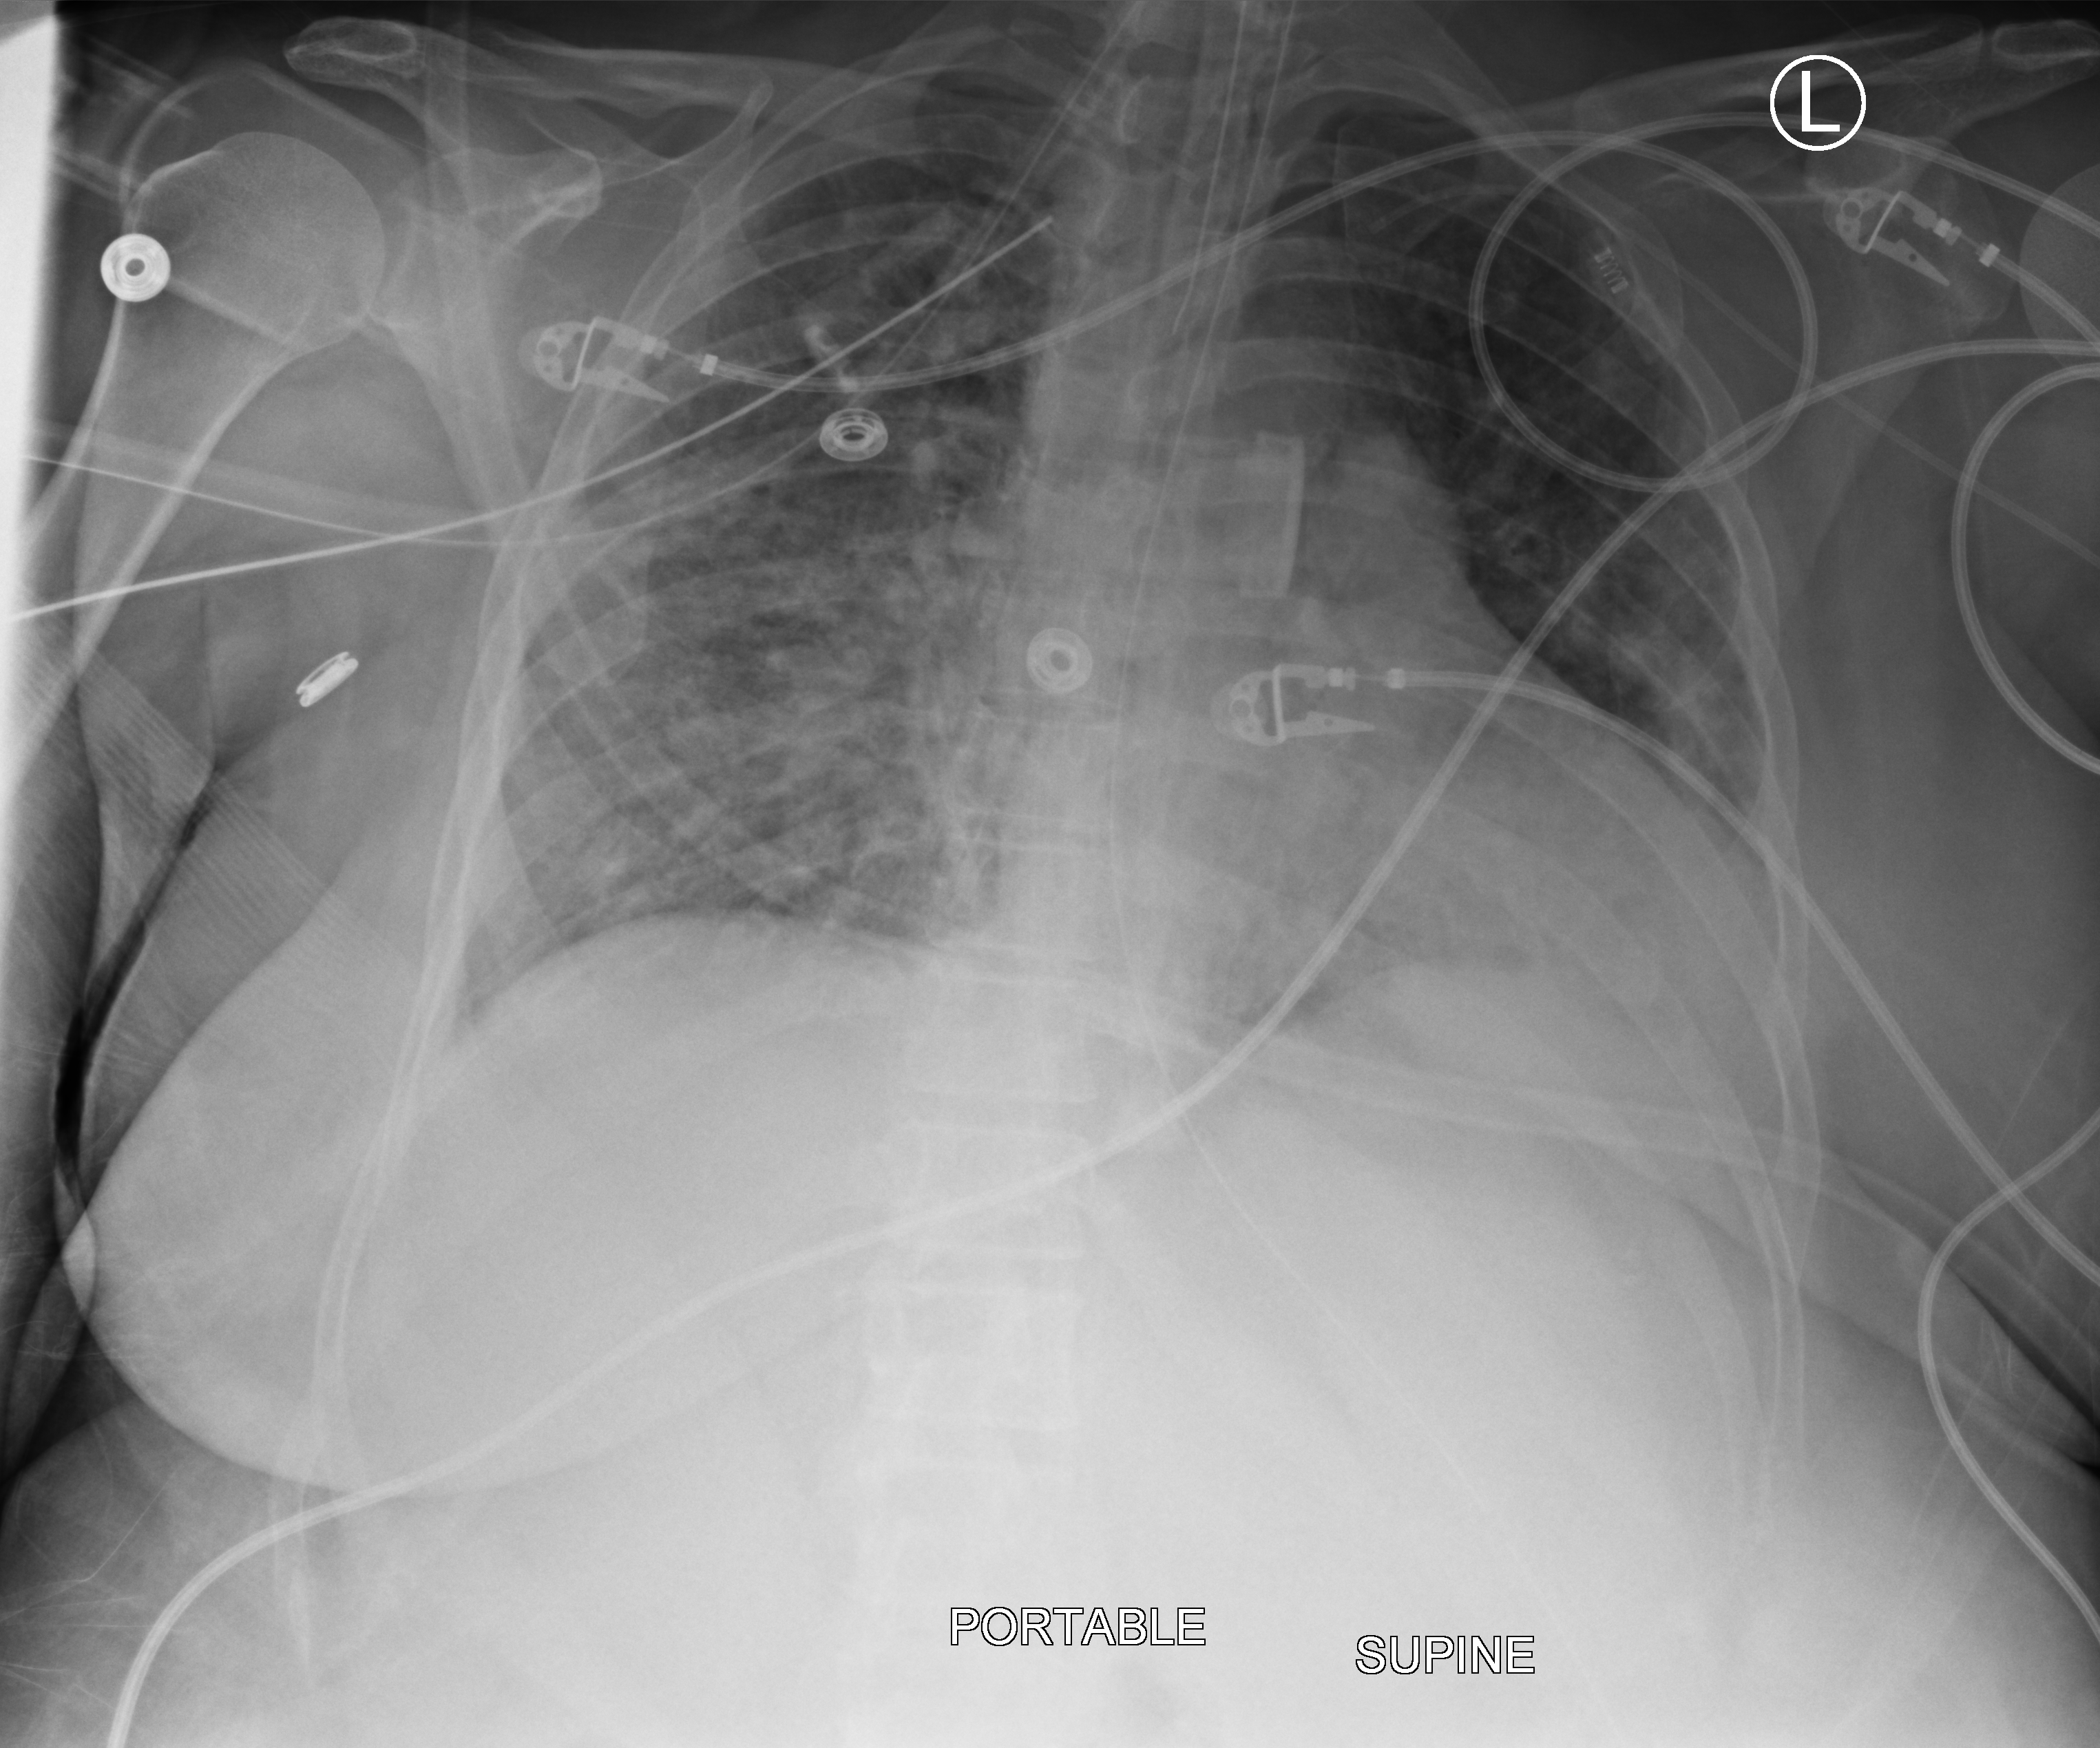
Chest X-ray (portable). Patient hospitalised with COVID-19; female, aged 18–59 years.
Hospital-stay facts (about this admission, not read from this image; timing relative to this image not recorded): diabetes (admission record): yes; admitted to intensive care during this hospital stay: yes.